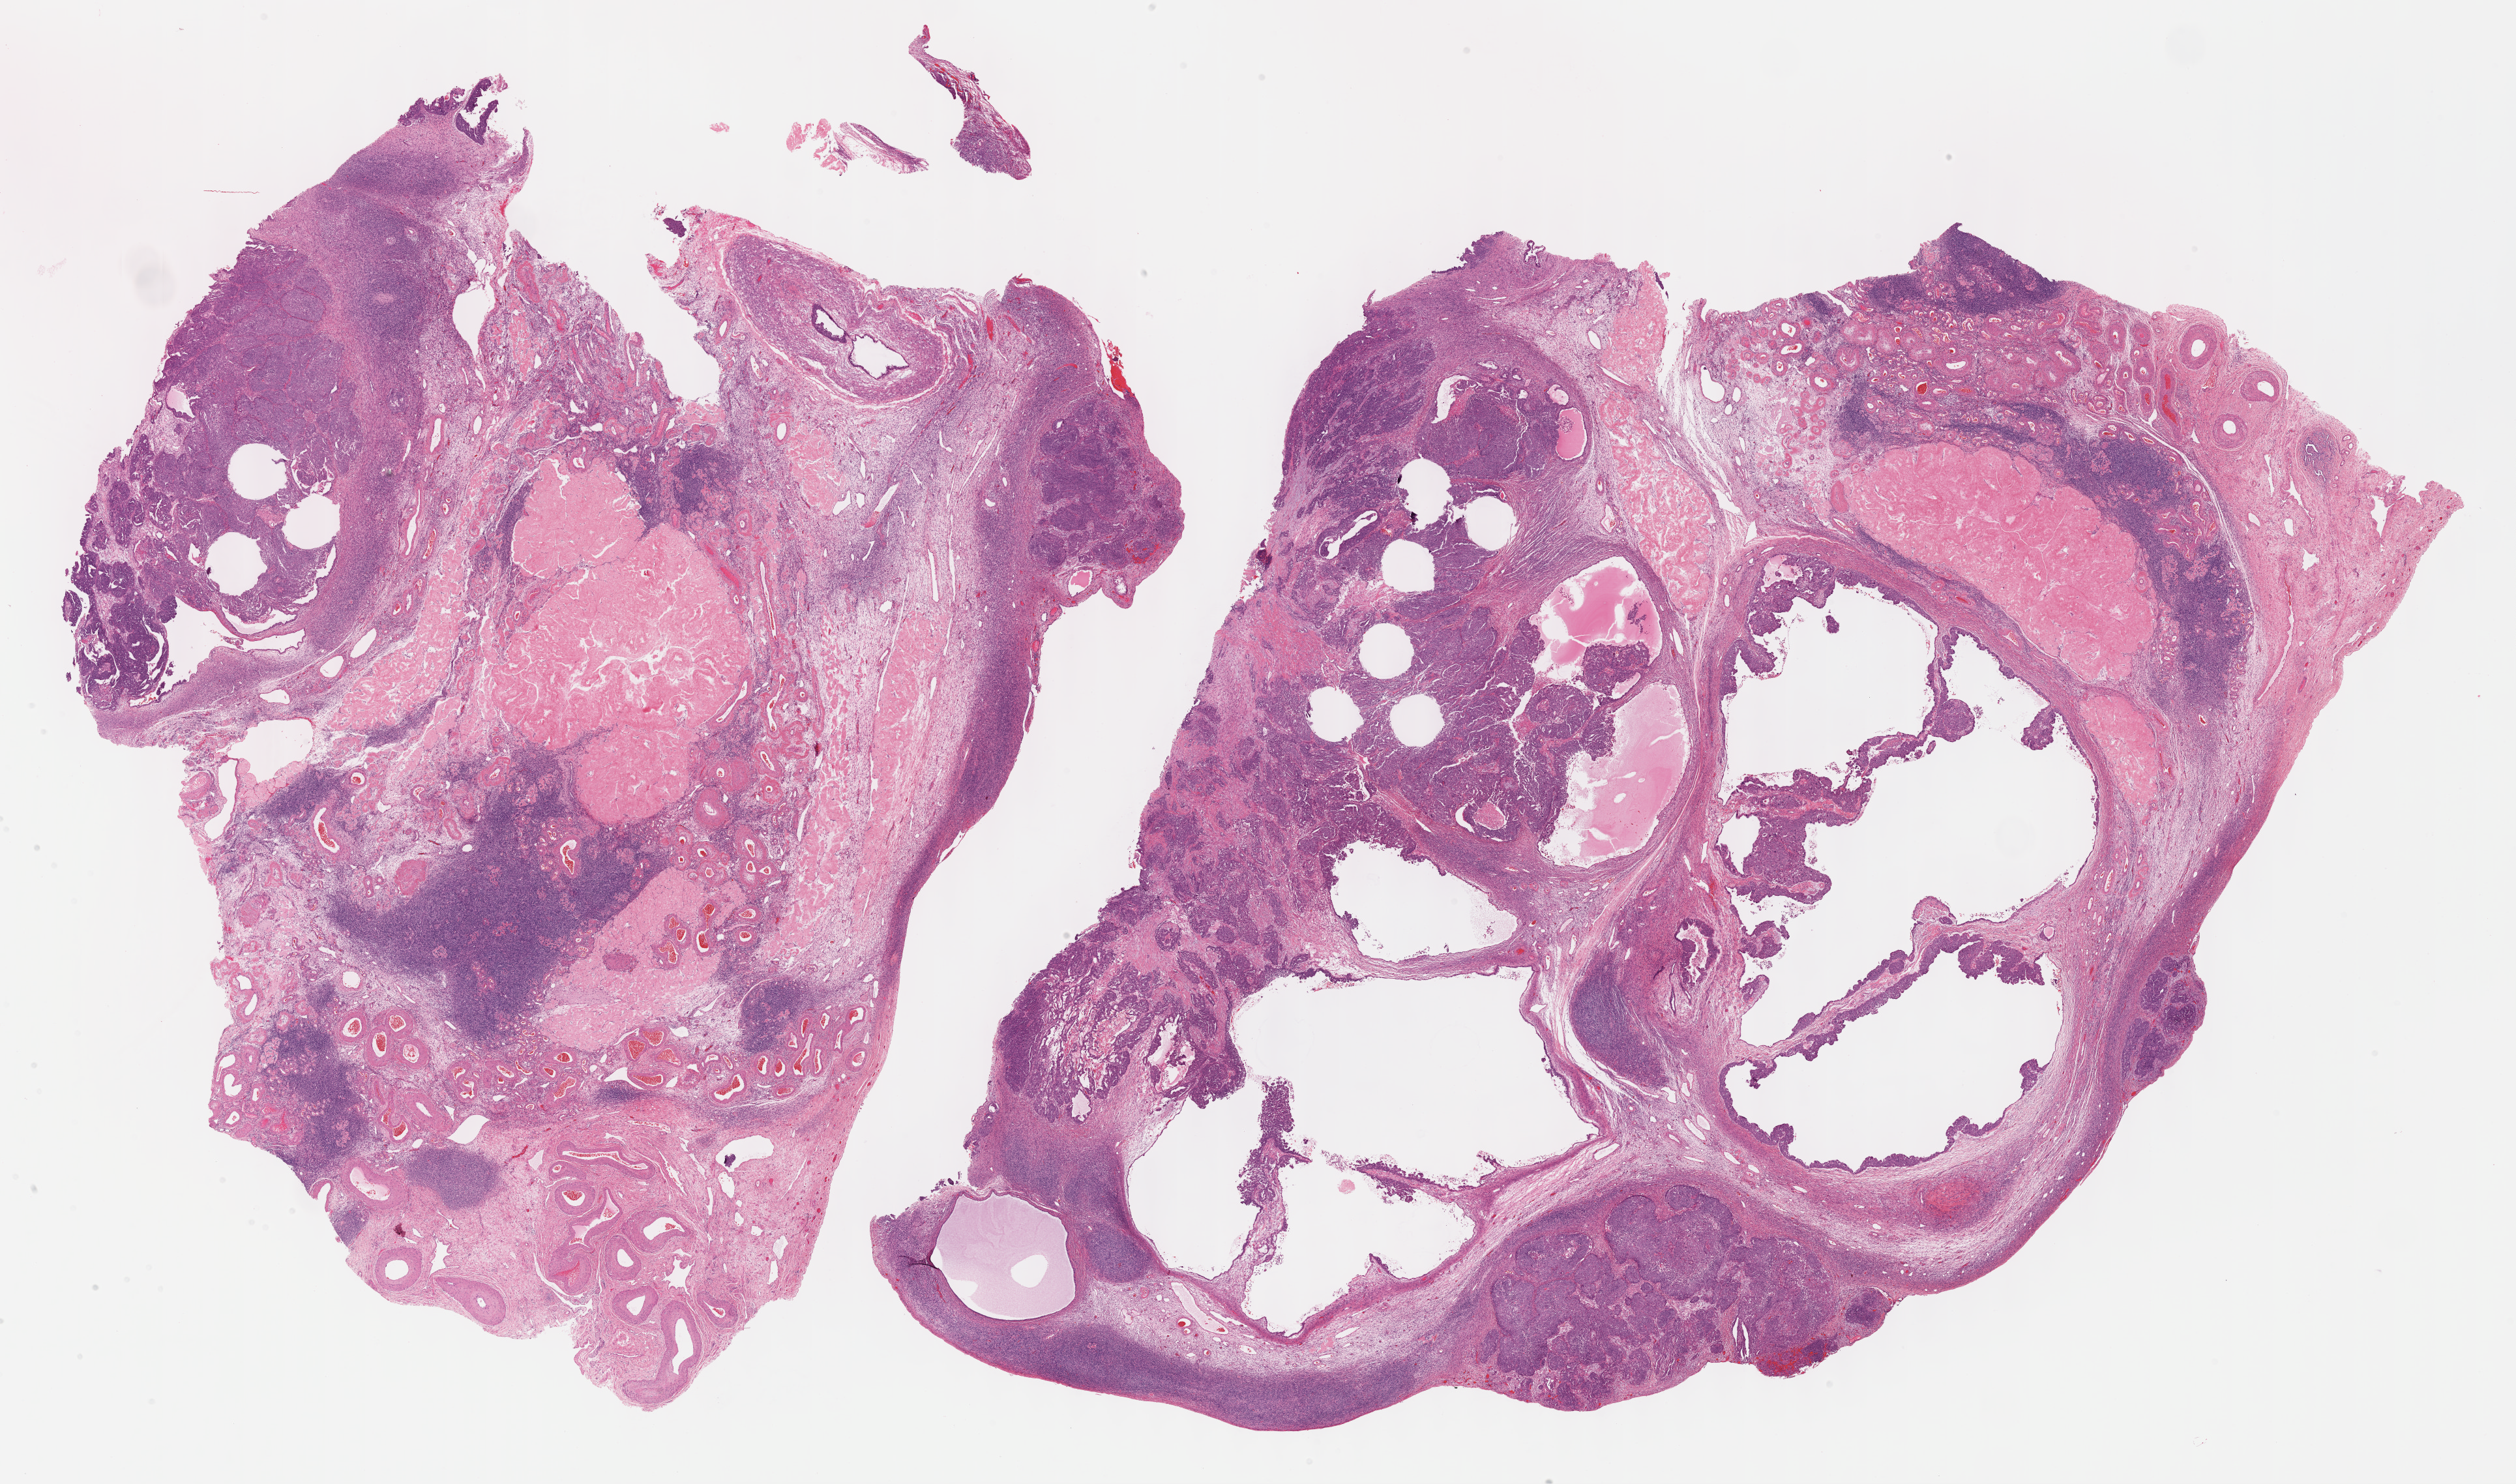
Digitized H&E-stained tissue section (whole slide), low-resolution overview of the scanned area, about 31.2 x 18.4 mm (slide scanned at 40x); formalin-fixed paraffin-embedded (FFPE) diagnostic section; sample: primary tumour, ovary. Female patient; age at initial diagnosis 60 years. Histologic grade: G3 (poorly differentiated).
* histologic diagnosis: Serous cystadenocarcinoma, NOS
* FIGO stage: IIIC